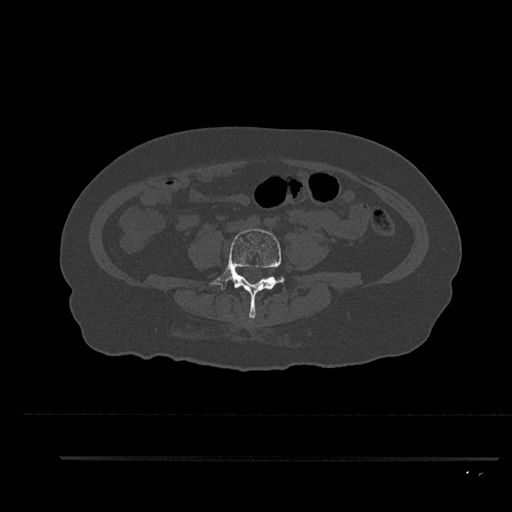
CT including the spine, one axial slice; position 18 of 797 along the scan axis; reconstruction kernel Br40s/3; bone window (W 1800 / L 400 HU); 512 × 512 image matrix, field of view 408 × 408 mm. Patient: female, 44 years. Case-level facts recorded for this patient, not image findings: primary cancer: renal.
Structures marked on this image (semi-automatically segmented with operator editing):
- L4 vertebra: box from (x=209, y=229) to (x=284, y=319) px